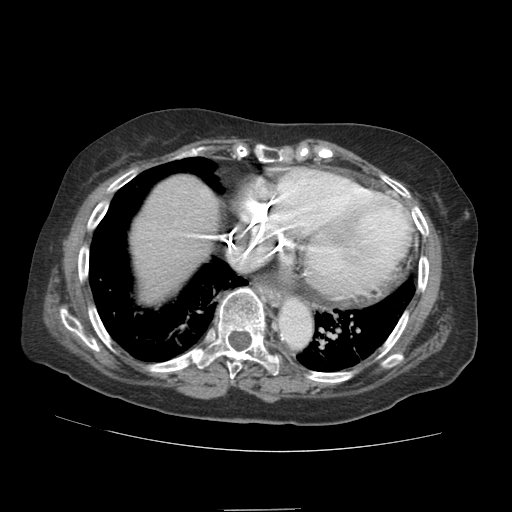
Contrast-enhanced abdominal CT (liver protocol), one axial slice; position 80 of 89 along the scan axis; 140 kVp; soft-tissue window (W 400 / L 40 HU); 2.5 mm slice thickness; 512 × 512 image matrix, field of view 360 × 360 mm. Case-level facts recorded for this patient, not image findings: diagnosis: hepatocellular carcinoma (patient treated with transarterial chemoembolisation; whether this scan precedes or follows treatment is not stated here); TNM stage (as recorded): Stage-II; Child-Pugh class: A.
Annotated regions visible in this slice (semi-automatically segmented with operator editing):
- abdominal aorta: bounding box [x1, y1, x2, y2] px = [280, 301, 310, 343]
- liver parenchyma outside the tumour (the mass and vessels are separate outlines, so this box may not span the whole liver): [130, 174, 218, 302]
- liver vessels: [188, 234, 212, 239]